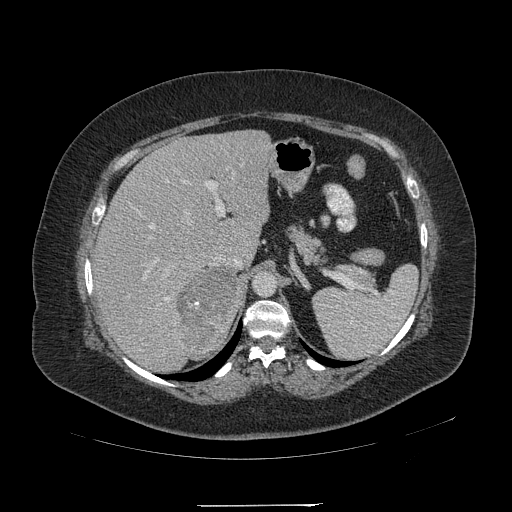
Contrast-enhanced abdominal CT, one axial slice; position 148 of 217 along the scan axis; 120 kVp; intravenous contrast given; soft-tissue window (W 400 / L 40 HU); 1.25 mm slice thickness; 512 × 512 image matrix. Female patient, age 55 years. Case-level facts recorded for this patient, not image findings: diagnosis: adrenocortical carcinoma; tumour side: right adrenal; tumour size at pathology: 11 cm; Ki-67 index: 20 %; stage (as recorded): 2.
Outlined on this slice (semi-automatically segmented with operator editing):
- mass: bounding box (x1, y1, x2, y2) in pixels: (177, 266, 238, 361)